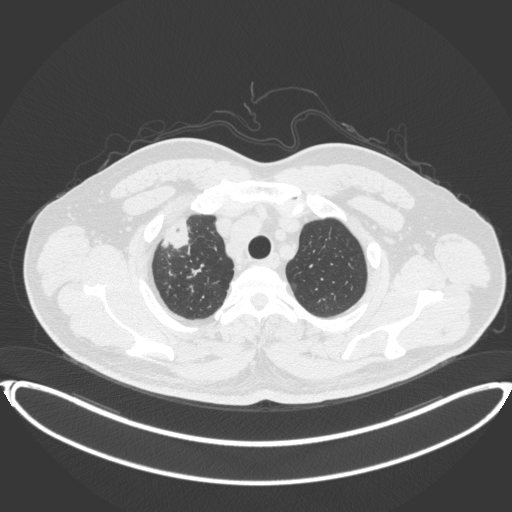
Chest CT, one axial slice; slice 336 of 399 in the series (ordered by position); lung window (W 1500 / L -600 HU); 1 mm slice thickness; 512 × 512 image matrix. Patient: male, 53 years. From the clinical record (not read from this slice): clinical TNM (as recorded): T2a N0 M0.
Structures marked on this image (bounding box drawn by a radiologist):
- lung tumour (recorded histology: adenocarcinoma): bounding box [x1, y1, x2, y2] px = [160, 213, 201, 252]